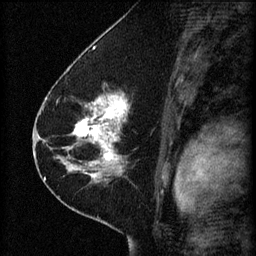
Breast MRI (dynamic contrast-enhanced), one sagittal slice; slice 35 of 60 in the series (ordered by position); 3 images stored at this slice position (order not interpretable as contrast timing); 1.5 T; TE 4.2 ms, TR 8.2 ms; 256 × 256 image matrix, field of view 180 × 180 mm. Patient: female, 41 years.
Structures marked on this image (semi-automatic segmentation, software-assisted and operator-edited):
- analysis volume of interest (the breast-tissue region the enhancement analysis was run in; not a lesion): bounding box <67,92,165,173> (left, top, right, bottom; pixels)
- tumour enhancement mask (voxels above the 70 % enhancement threshold inside the analysis volume of interest): <67,94,128,173>